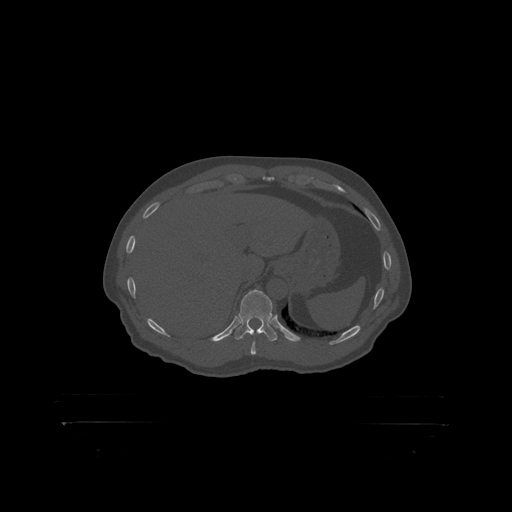
CT including the spine, one axial slice; slice 383 of 399 in the series (ordered by position); reconstruction kernel STANDARD; 120 kVp; bone window (W 1800 / L 400 HU); 512 × 512 image matrix. Male patient, age 46 years. From the clinical record (not read from this slice): primary cancer: skin.
Annotated regions visible in this slice (semi-automatic segmentation, software-assisted and operator-edited):
- T11 vertebra: bounding box [x1, y1, x2, y2] px = [239, 291, 273, 319]